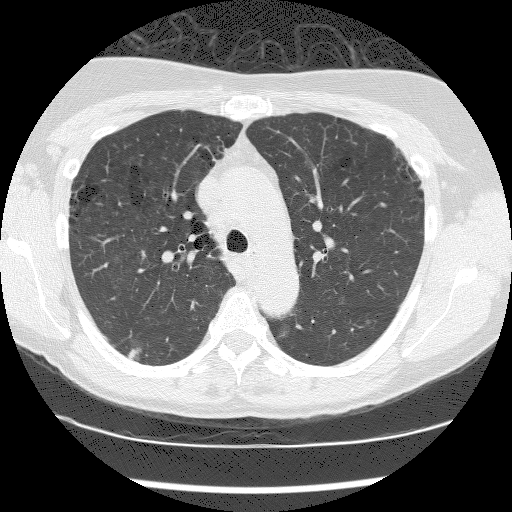
Low-dose screening chest CT, one axial slice; slice 128 of 176 in the series (ordered by position); reconstruction kernel BONE; 120 kVp; lung window (W 1500 / L -600 HU); 2.5 mm slice thickness; 512 × 512 image matrix, field of view 320 × 320 mm.
Outlined on this slice (outlined manually by an expert reader):
- lesion 1 (tumor, lower lobe of right lung): box from (x=129, y=348) to (x=141, y=360) px